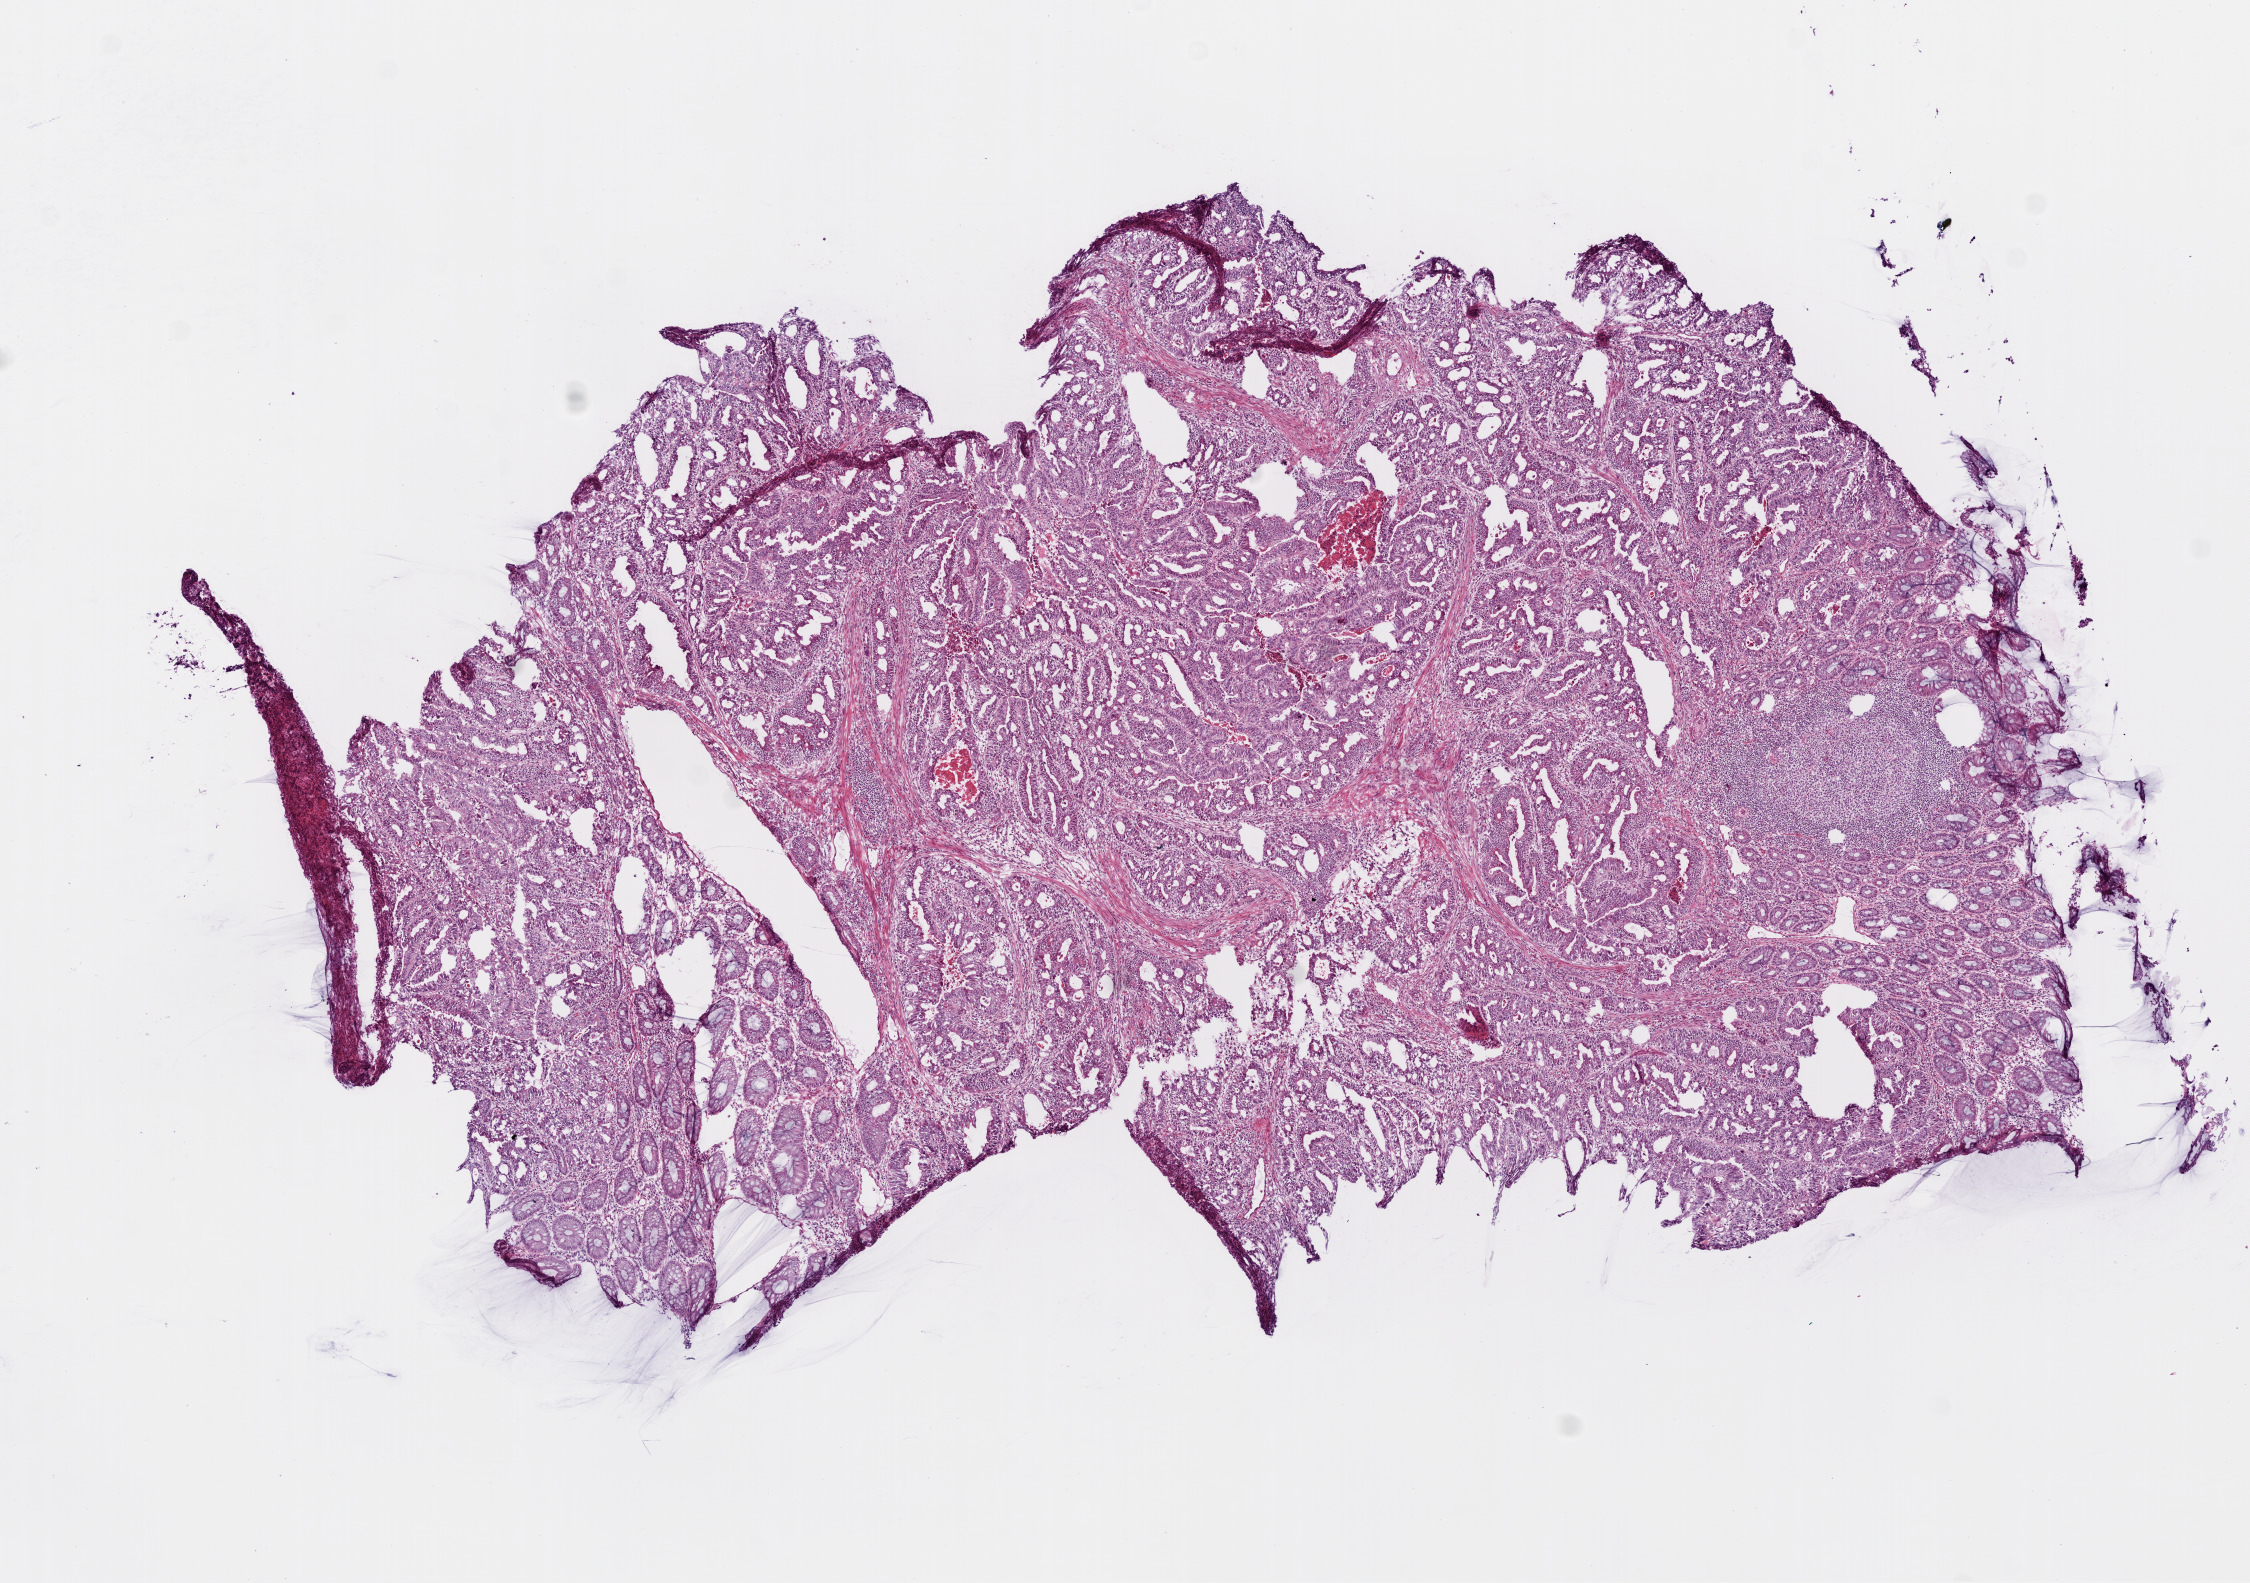
Whole-slide histology image, H&E — low-resolution overview of the scanned area, about 9.0 x 6.4 mm (slide scanned at 20x); frozen section; sample: primary tumour, colon. Male patient; age at initial diagnosis 66 years. Slide review estimates, as recorded: tumour cells 72%, tumour nuclei 75%, normal cells 10%, stromal cells 10%, necrosis 8%.
AJCC pathologic stage: IIA. Lymph nodes positive (case pathology): 0 of 24 examined. TNM: T3 N0 M0. Diagnosis: Adenocarcinoma, NOS.